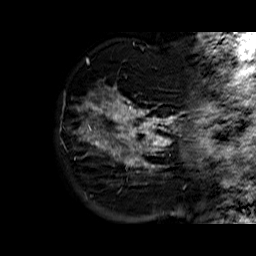
Breast MRI (dynamic contrast-enhanced), one sagittal slice. Position 12 of 60 along the scan axis. Dynamic contrast-enhanced series, time point 2 of 6 at this slice position (early post-contrast). 1.5 T. TE 6.3 ms, TR 32.4 ms. 4 mm slice thickness. 256 × 256 image matrix, field of view 200 × 200 mm. Female patient. Case-level facts recorded for this patient, not image findings: setting: breast cancer imaged before/during neoadjuvant chemotherapy; receptor status: HR-positive, HER2-negative.
Outlined on this slice (semi-automatically segmented with operator editing):
- analysis volume of interest (the breast-tissue region the enhancement analysis was run in; not a lesion): bounding box [x1, y1, x2, y2] px = [75, 76, 177, 183]
- tumour enhancement mask (voxels above the 100 % enhancement threshold inside the analysis volume of interest): [79, 86, 177, 173]